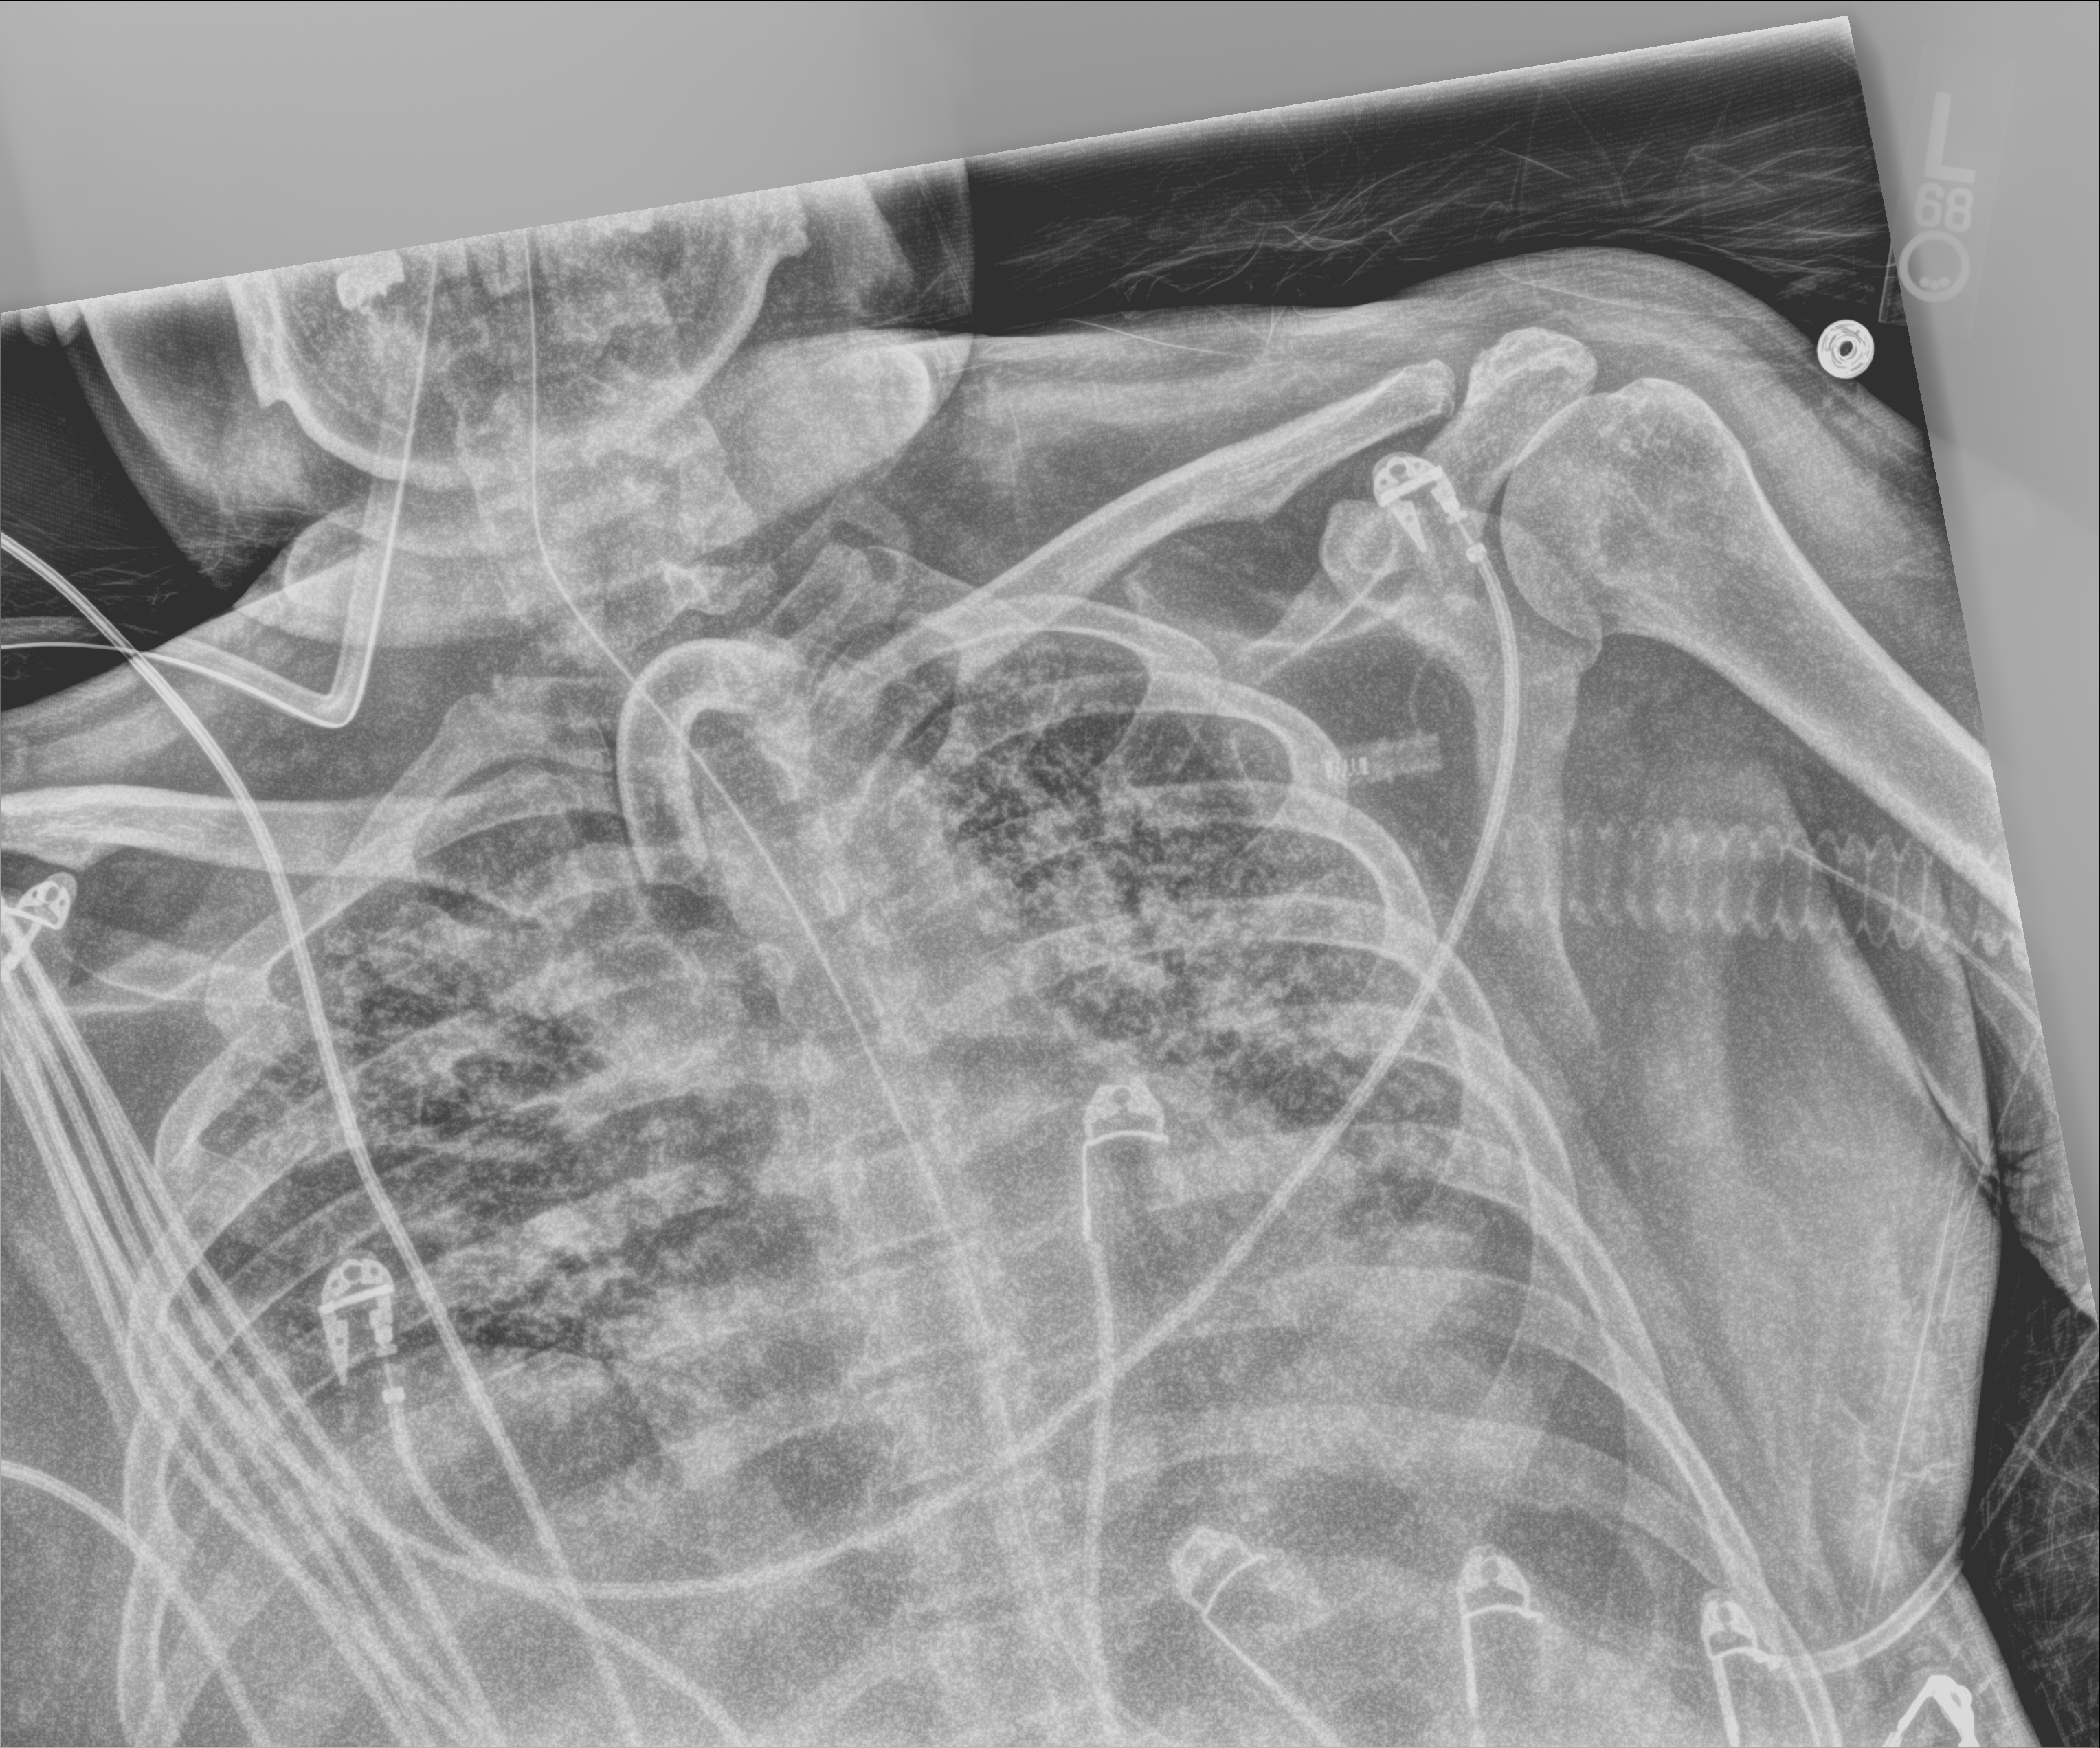
Bedside chest radiograph (computed radiography), anteroposterior (AP) projection. Patient hospitalised with COVID-19; male, aged 18–59 years.
Admission-level facts for this patient (not findings on this image; timing relative to this image not recorded):
- smoking status (admission record): never
- diabetes (admission record): no
- COPD (admission record): no